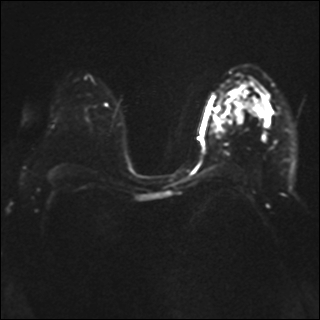
Breast MRI, one axial slice. Slice 24 of 41 in the series (ordered by position). Diffusion-weighted series; image 2 of 4 stored at this slice position (different b-values; order by instance number). 1.5 T. 320 × 320 image matrix, field of view 340 × 340 mm. Female patient.
Outlined on this slice (manually delineated by an expert):
- tumour on diffusion-weighted imaging: bounding box (x1, y1, x2, y2) in pixels: (229, 112, 245, 125)